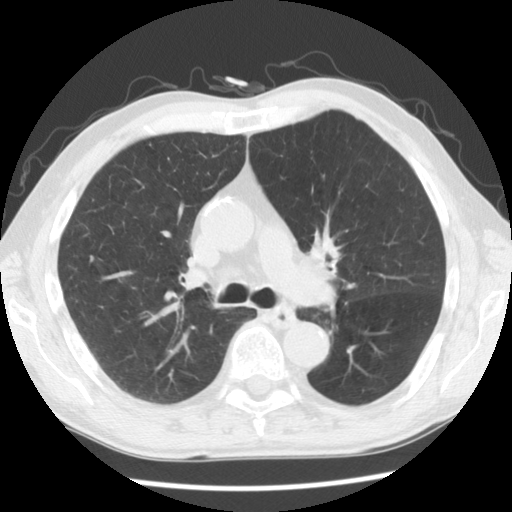
Low-dose screening chest CT, axial slice, baseline screening round, lung window (W 1500 / L -600 HU), 2.5 mm slice thickness, 140 kVp, slice 80 of 132 in the series. Male, age 68 years at enrolment. Current smoker at enrolment.
Expert-annotated lung lesion, bounding box [x1, y1, x2, y2] px = [296, 226, 355, 280]. No non-calcified nodule or mass ≥4 mm was recorded by the screening reader at this exam. Official screen result: negative screen, minor abnormalities not suspicious for lung cancer. Later outcome: lung cancer diagnosed 215 days after this screen — squamous cell carcinoma, NOS, left hilum, stage IIB (AJCC 6th edition), 32 mm at pathology.